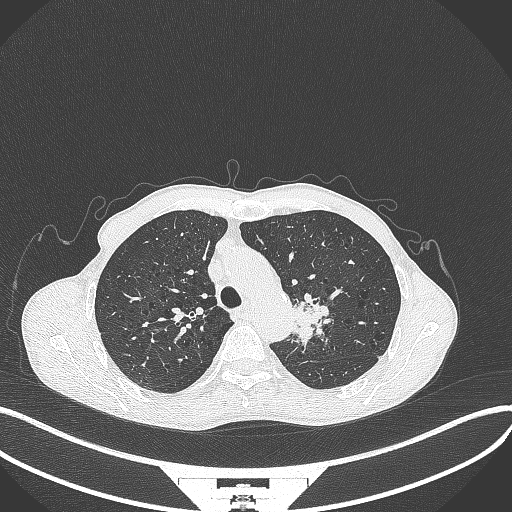
Chest CT, one axial slice; 120 kVp; lung window (W 1500 / L -600 HU); 512 × 512 image matrix. Patient: male, 65 years. Case-level facts recorded for this patient, not image findings: clinical TNM (as recorded): T2b N0 M0.
Outlined on this slice (bounding box drawn by a radiologist):
- lung tumour (recorded histology: adenocarcinoma): bounding box (x1, y1, x2, y2) in pixels: (292, 284, 330, 350)